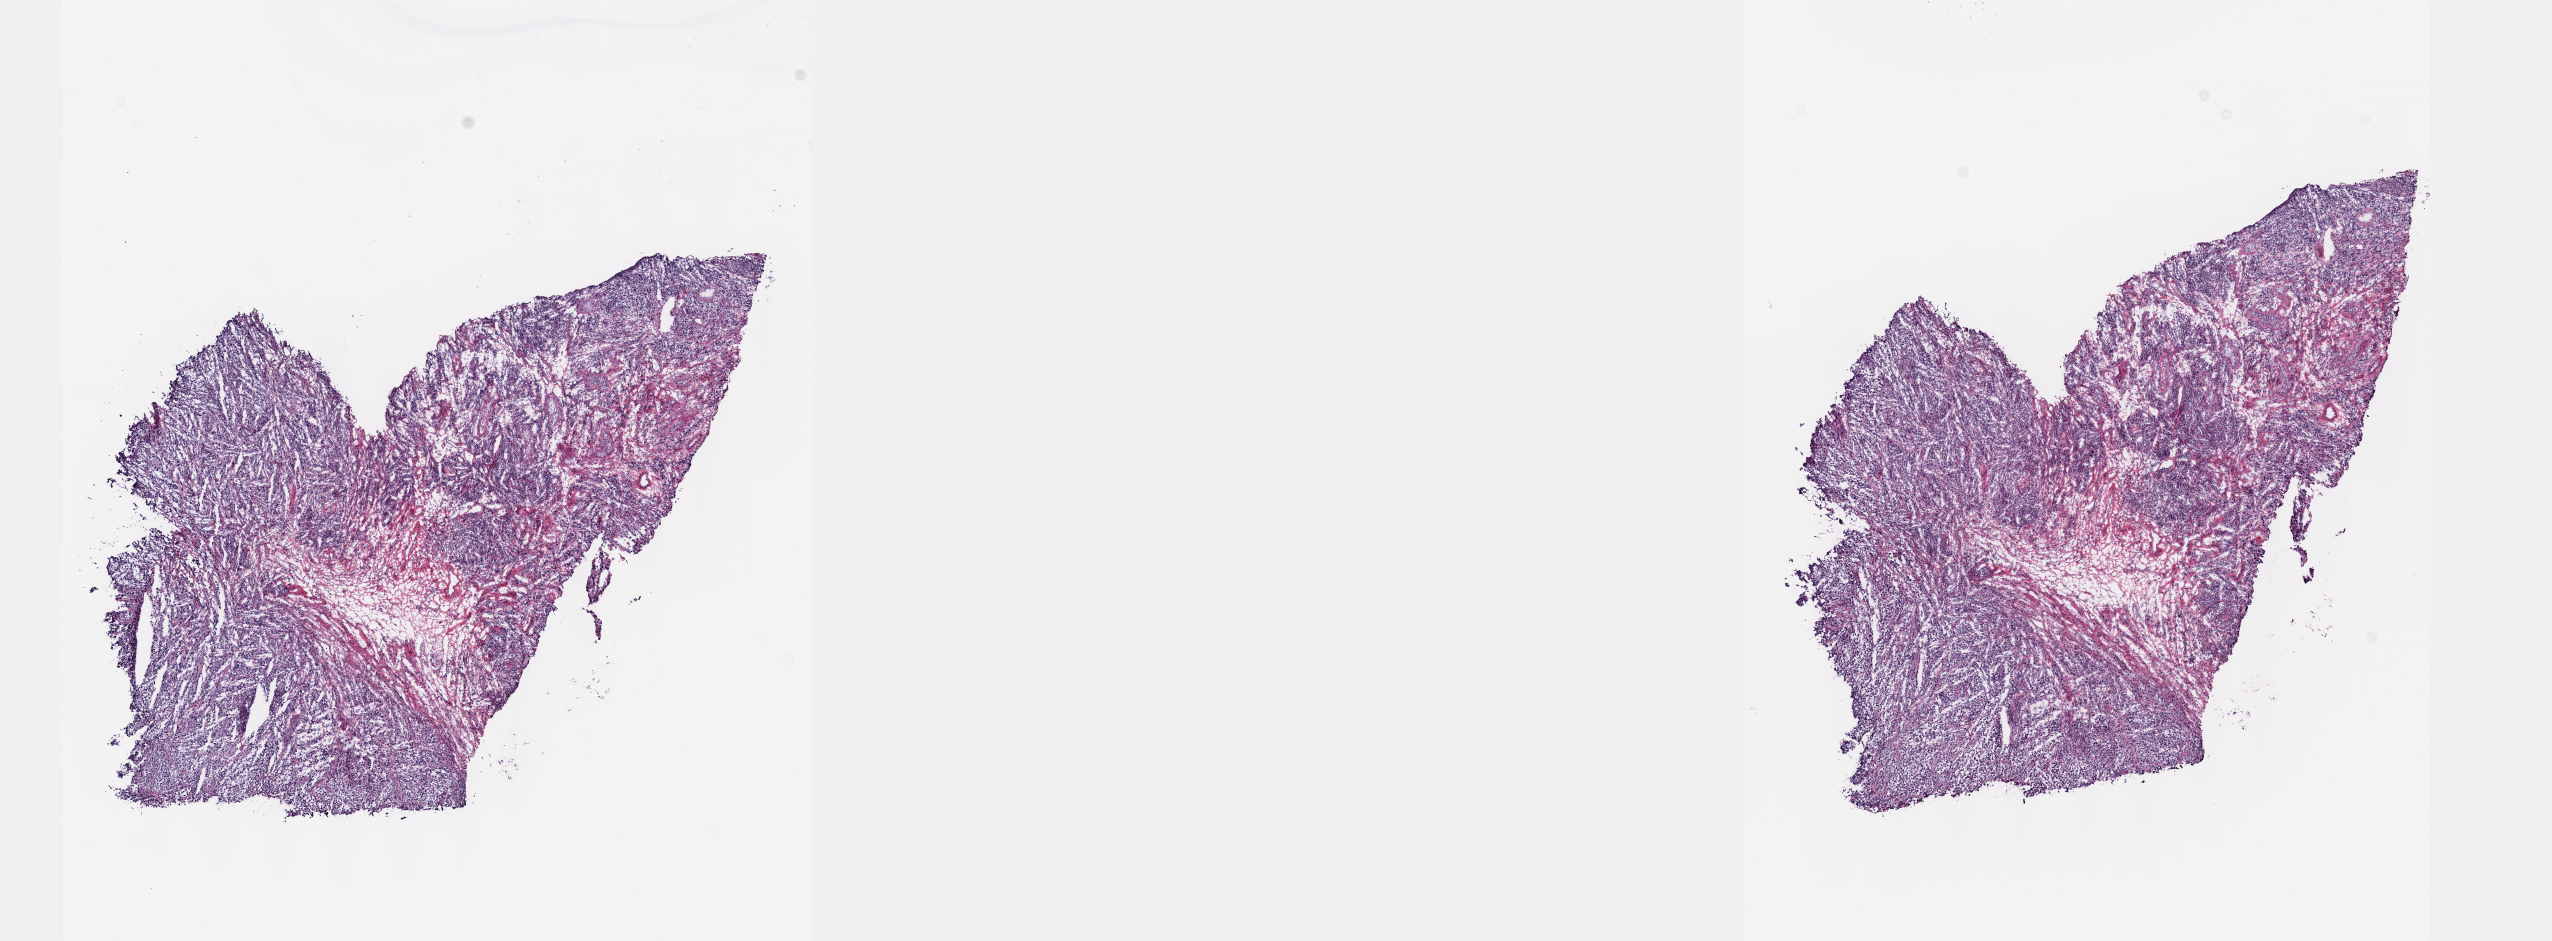
Hematoxylin and eosin (H&E) stained whole-slide image, low-resolution overview of the scanned area, about 20.6 x 7.6 mm (acquisition: 40x scan). Frozen section. Primary tumour sample from the testis. Male, age 27 years at initial diagnosis. Pathologist review of this section (percent, as recorded): tumour cells 80%, tumour nuclei 95%, normal cells 0%, stromal cells 10%, necrosis 10%. Inflammatory infiltration, as recorded: lymphocyte infiltration 0%, monocyte infiltration 0%, neutrophil infiltration 0%.
Histologic diagnosis: Seminoma, NOS. AJCC pathologic stage: I (7th edition).